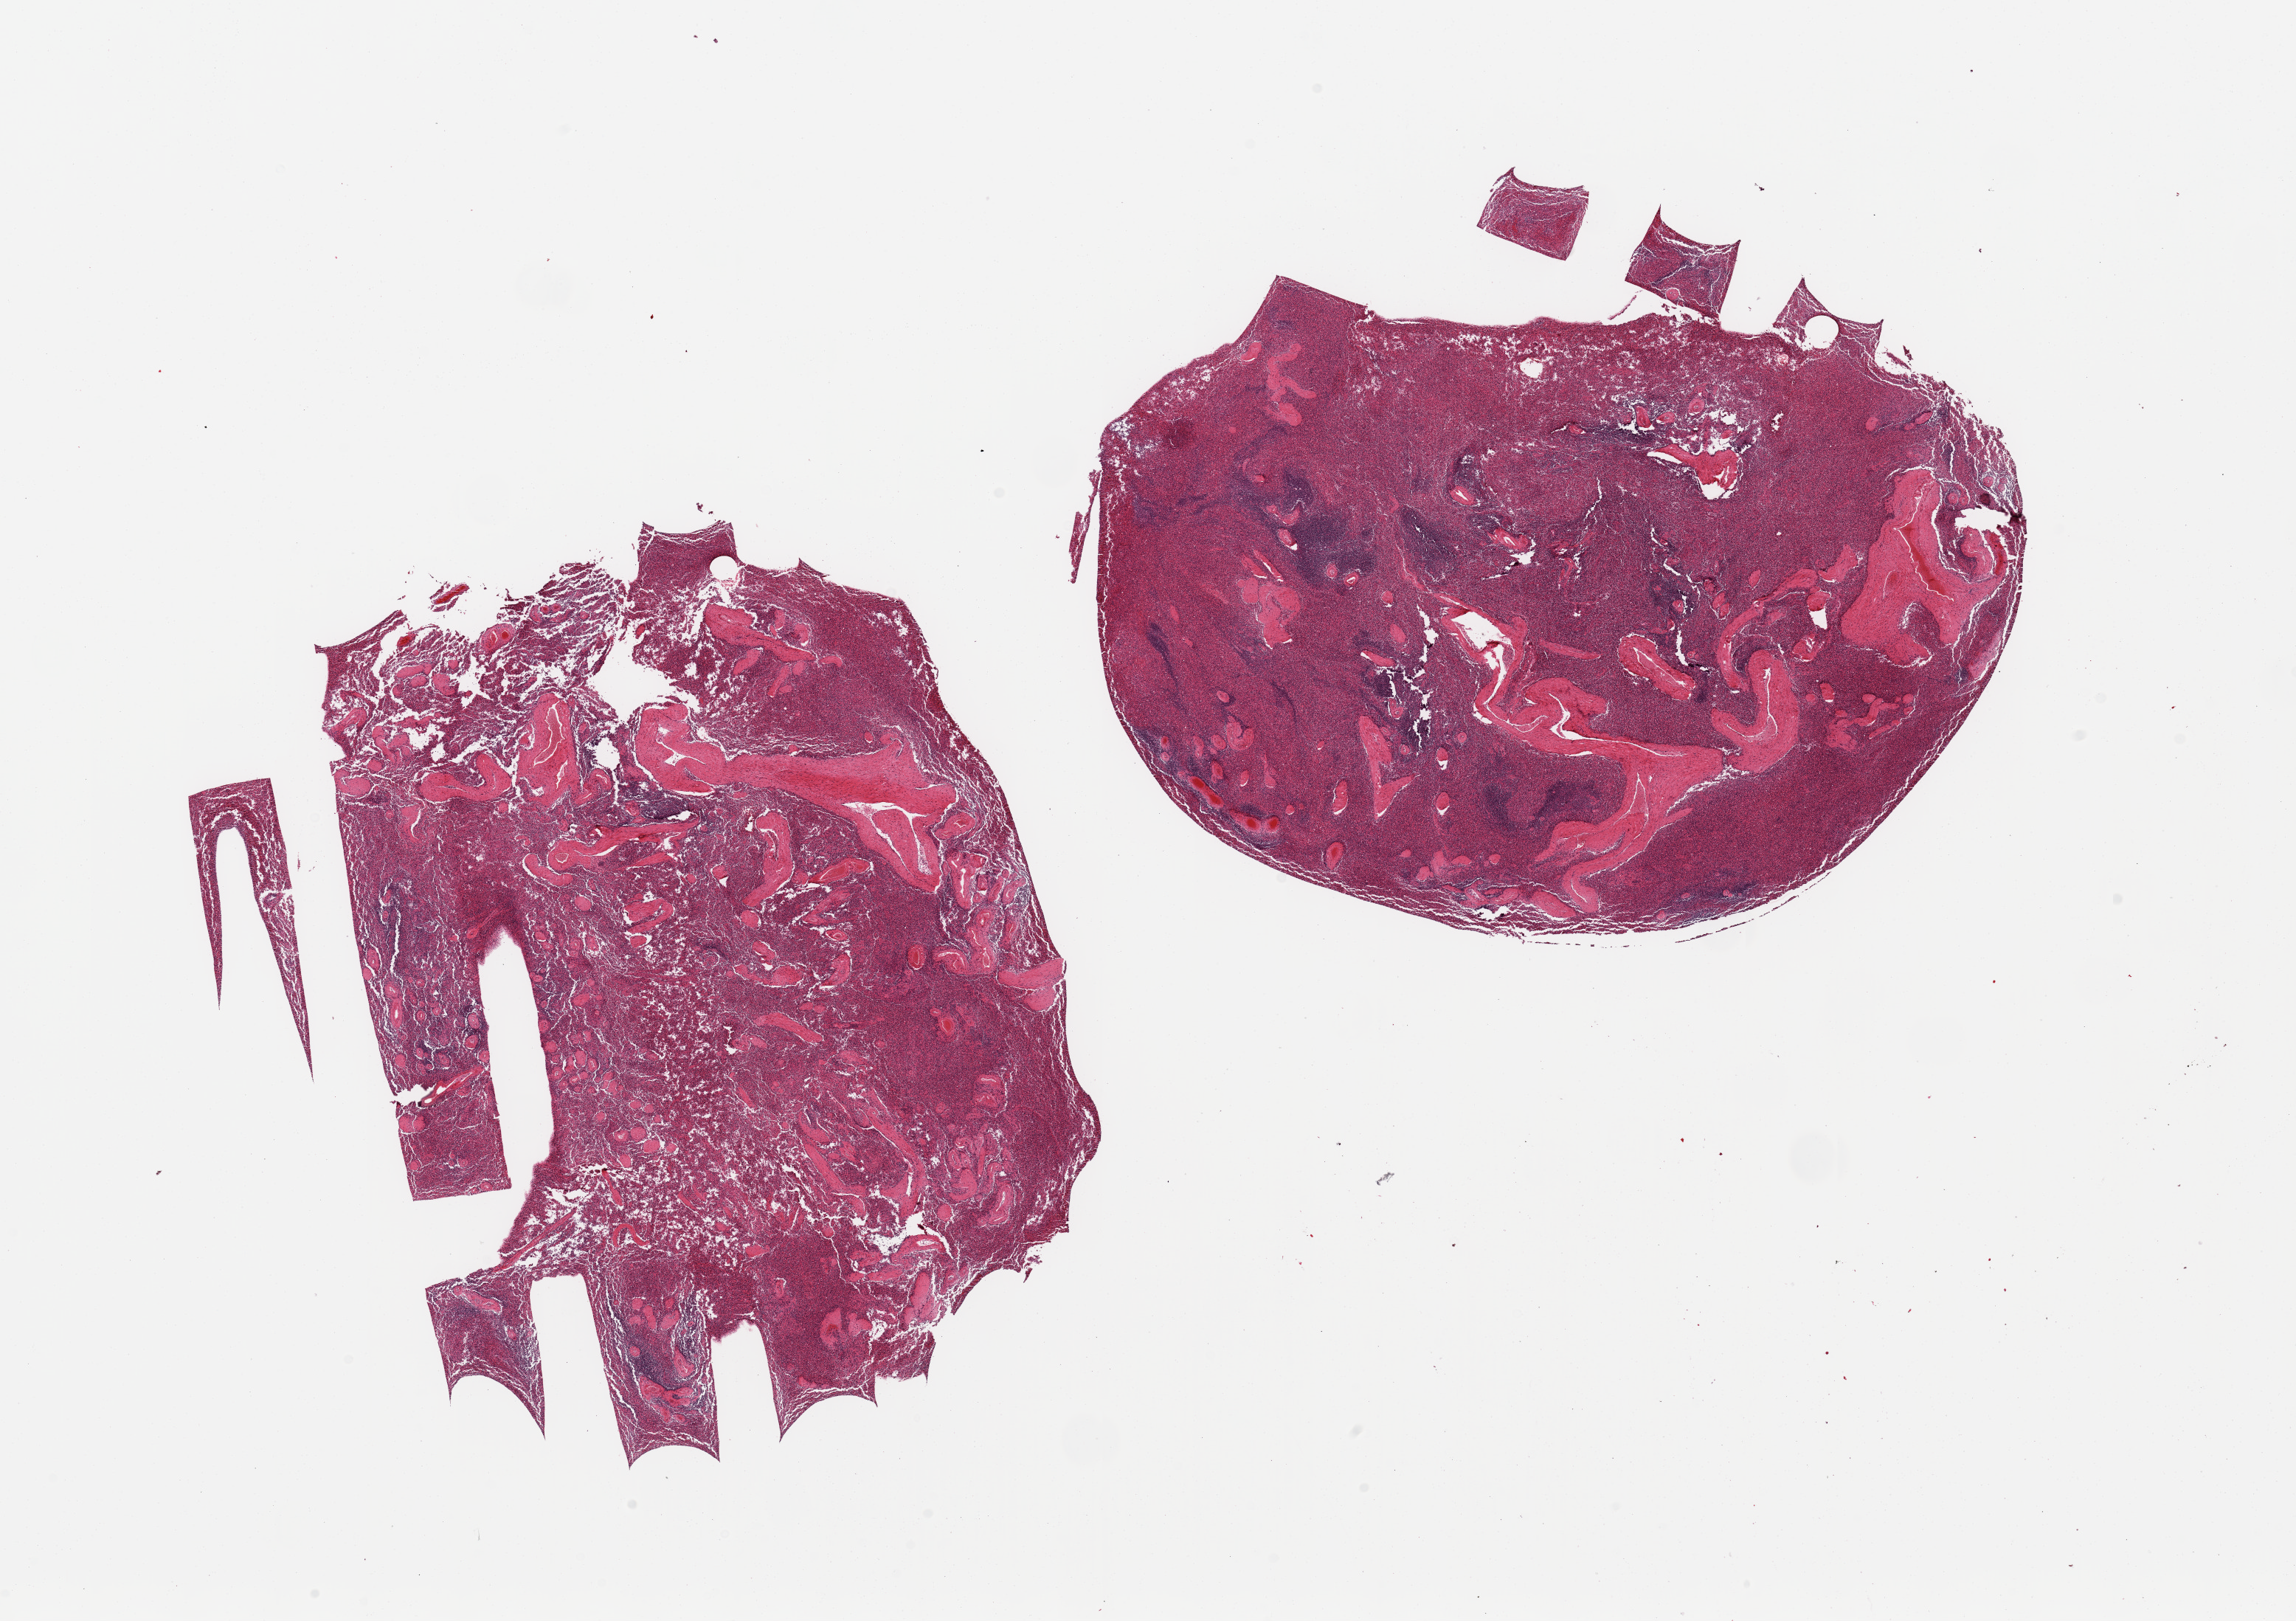
Whole-slide image, haematoxylin and eosin stain, brightfield, a low-resolution overview of the entire scanned area, about 24.6 x 17.4 mm, PAXgene-fixed paraffin-embedded (PFPE) section, target tissue: spleen, donor tissue sample. Donor: female.
- reviewer comment on this tissue sample: 2 pieces